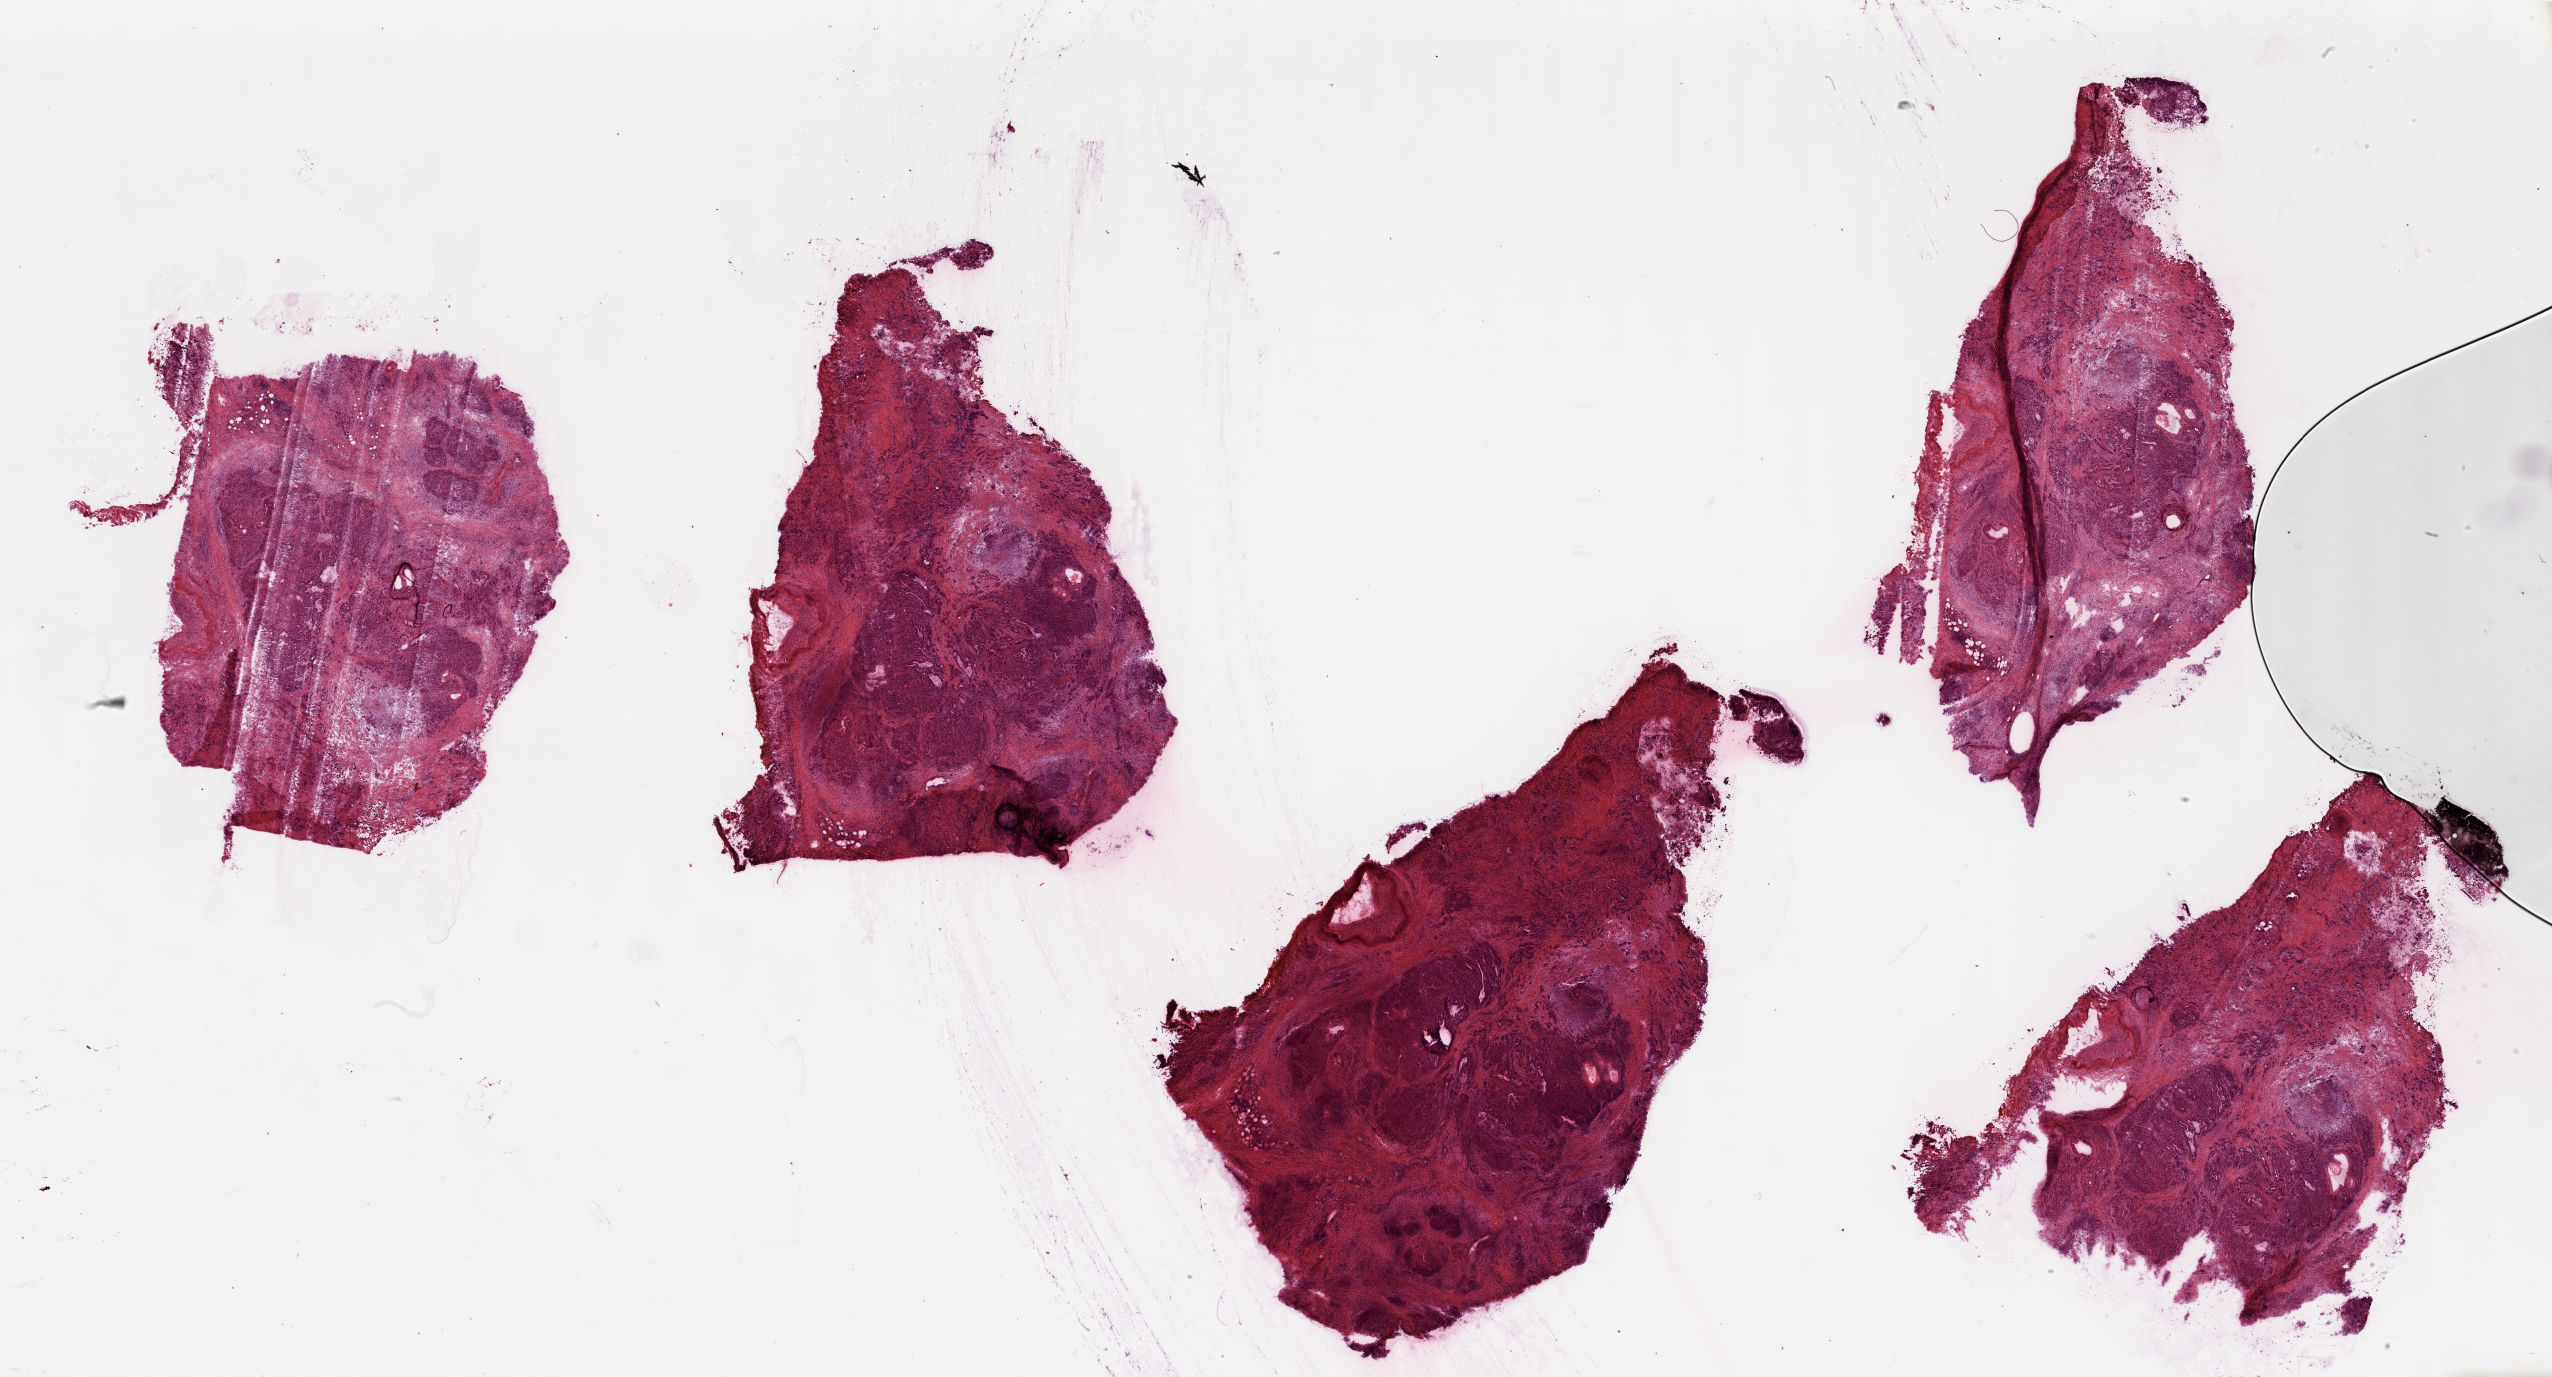
Digitized Hematoxylin and eosin (H&E) stained tissue section (whole slide), whole scanned area (about 40.4 x 21.8 mm) shown as a low-resolution overview. Tumour tissue sample, pancreas. Patient: male, age 58 years. Histologic grade: G3 (poorly differentiated).
• AJCC pathologic stage: IV
• primary tumour site (as recorded): head
• histologic diagnosis: Infiltrating duct carcinoma, NOS